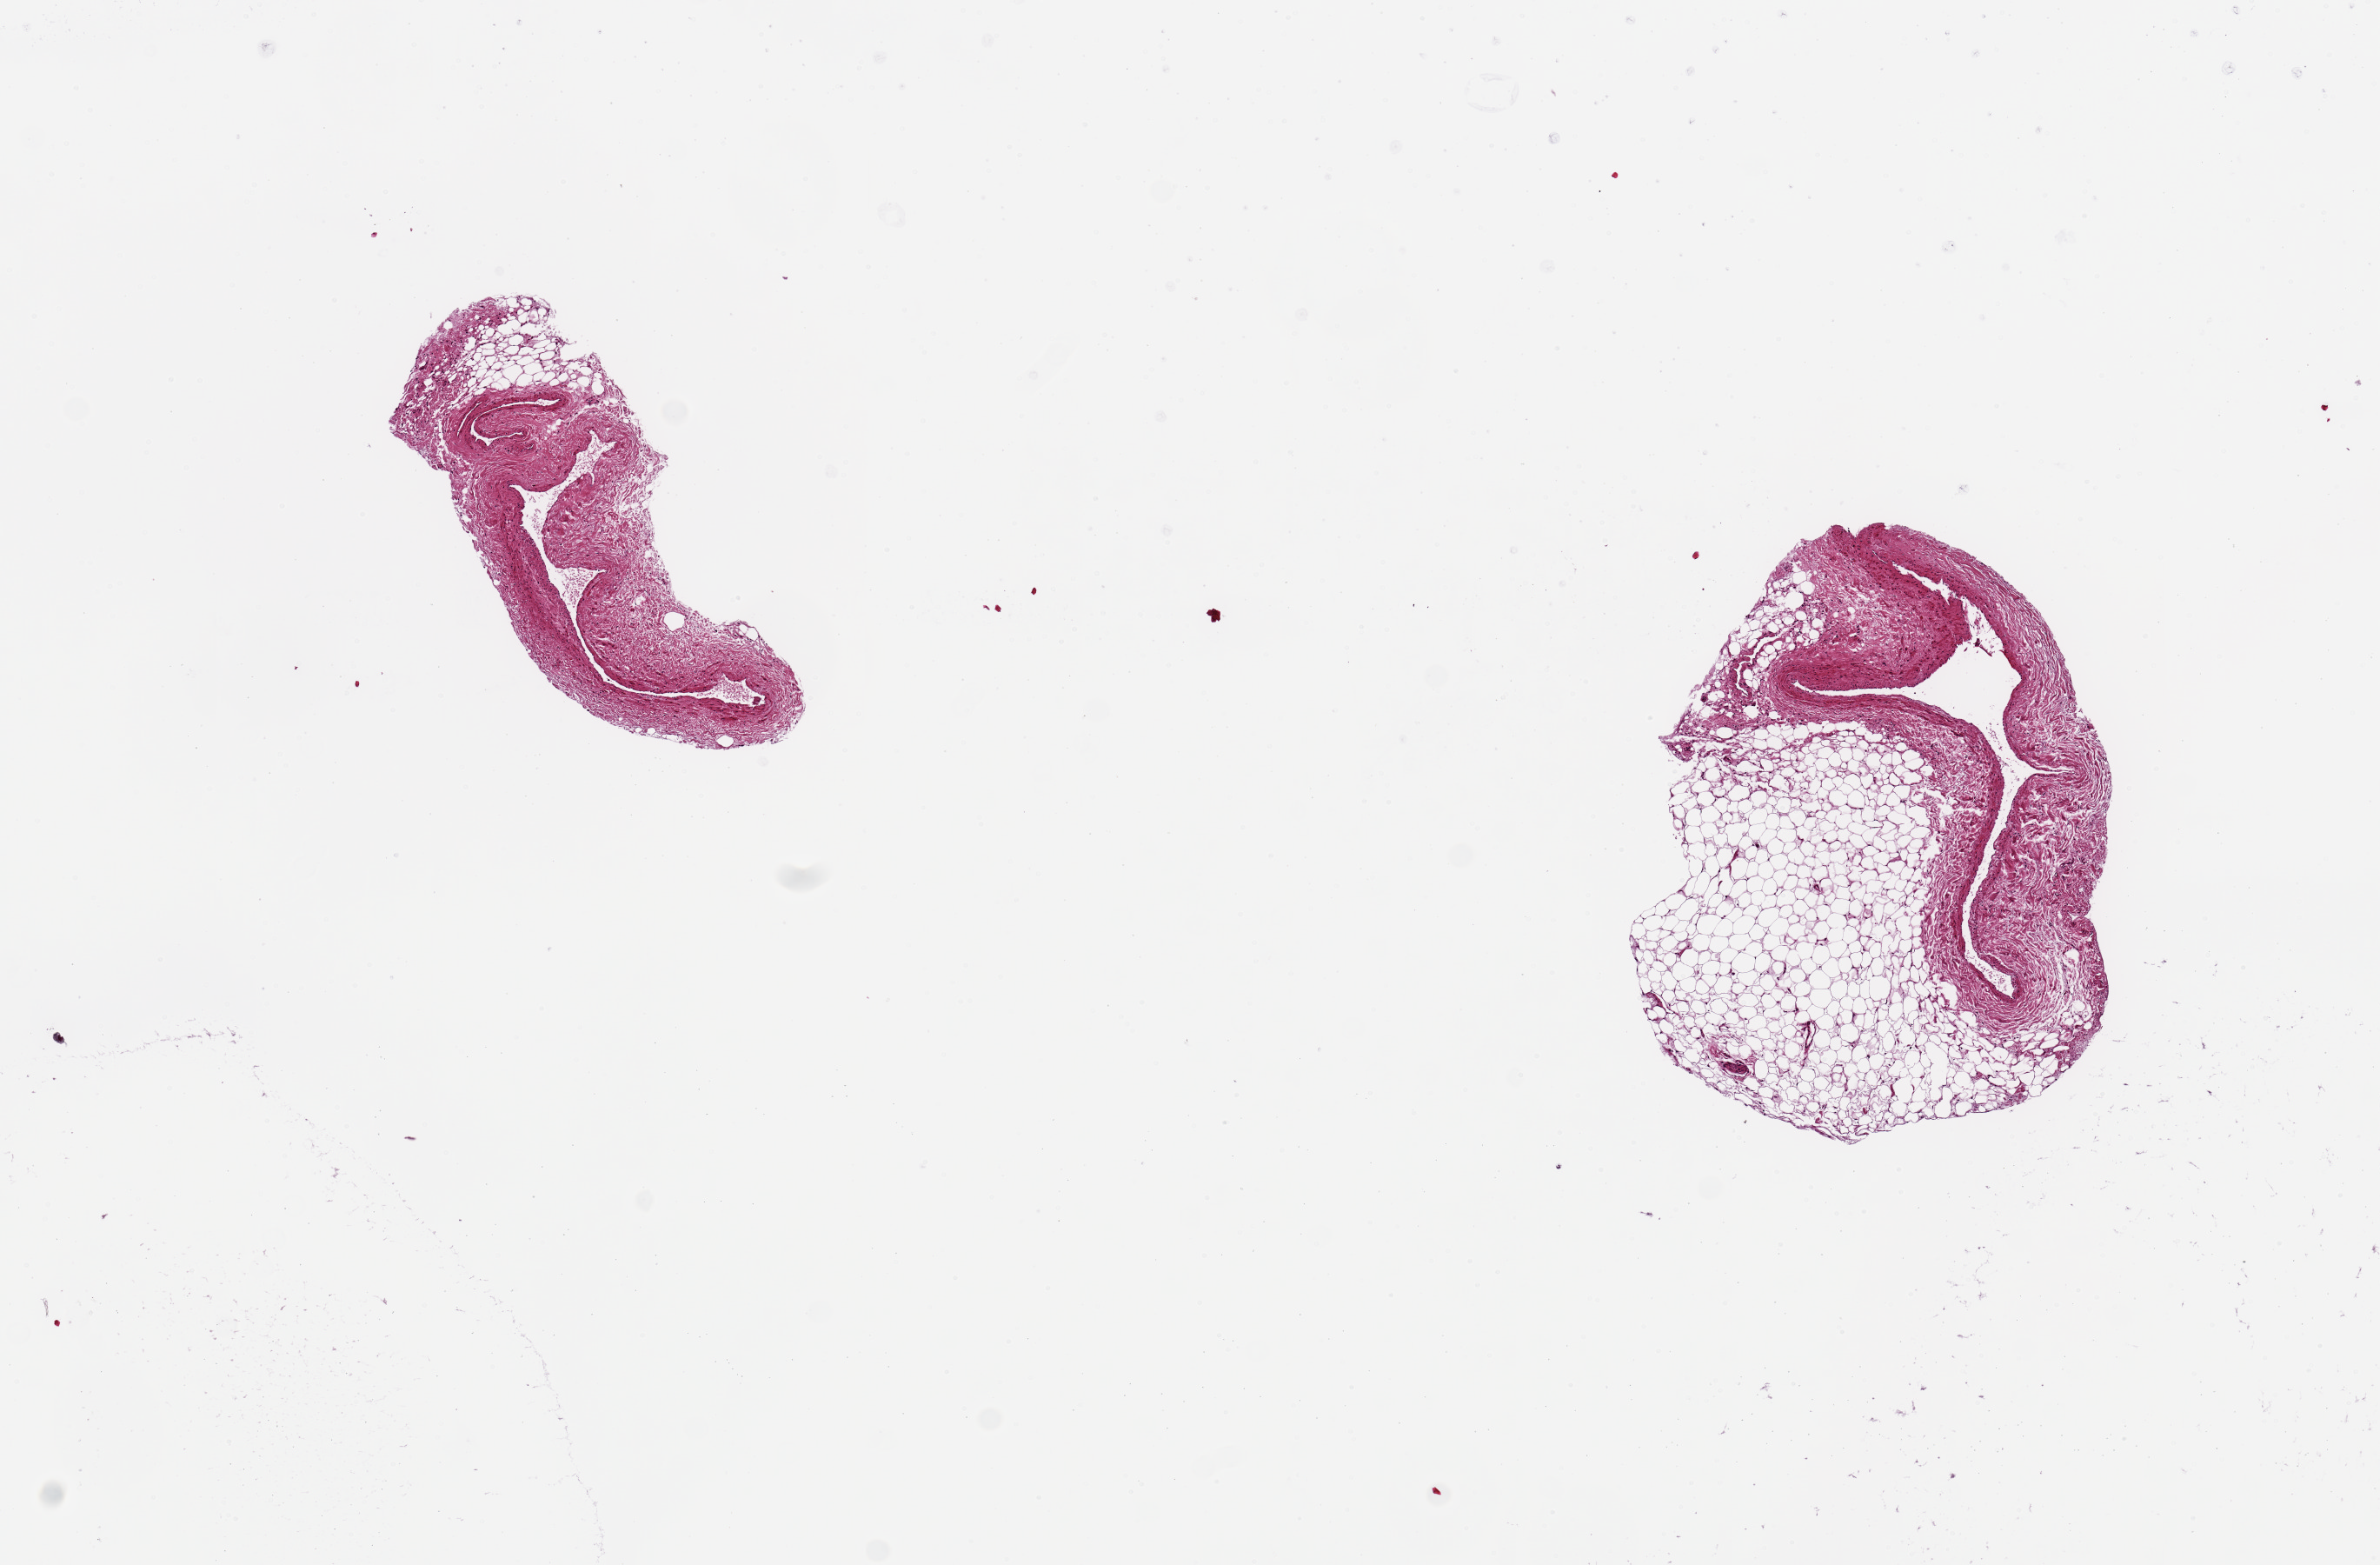
Haematoxylin and eosin whole-slide image — low-resolution overview of the scanned area, about 10.8 x 7.1 mm (acquisition: 20x scan), PAXgene-fixed paraffin-embedded (PFPE) section, target tissue: coronary artery, donor tissue sample.
Review note (as recorded): 2 ~2mm d sections, one with approximately equal amount of fat on edge (~2x2mm).